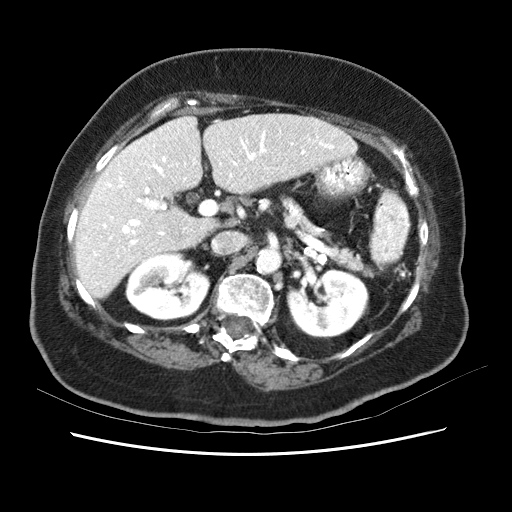
Contrast-enhanced abdominal CT (liver protocol), one axial slice. Soft-tissue window (W 400 / L 40 HU). 2.5 mm slice thickness. 512 × 512 image matrix, field of view 340 × 340 mm. Case-level facts recorded for this patient, not image findings: diagnosis: hepatocellular carcinoma (patient treated with transarterial chemoembolisation; whether this scan precedes or follows treatment is not stated here); TNM stage (as recorded): Stage-I; Child-Pugh class: B; tumour nodularity: uninodular.
Structures marked on this image (semi-automatically segmented with operator editing):
- liver parenchyma outside the tumour (the mass and vessels are separate outlines, so this box may not span the whole liver): box from (x=74, y=112) to (x=358, y=300) px
- liver vessels: (x=78, y=117)–(x=354, y=282)